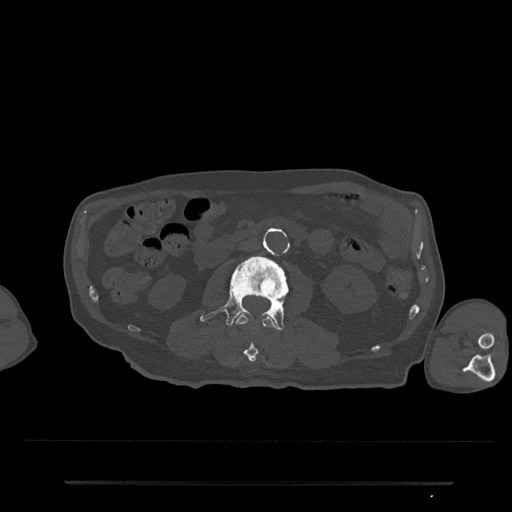
CT including the spine, one axial slice; reconstruction kernel Br40s/3; 120 kVp; bone window (W 1800 / L 400 HU); 0.5 mm slice thickness; 512 × 512 image matrix, field of view 427 × 427 mm. Male patient, age 74 years. From the clinical record (not read from this slice): primary cancer: prostate.
Outlined on this slice (semi-automatically segmented with operator editing):
- L2 vertebra: bounding box (x1, y1, x2, y2) in pixels: (234, 314, 279, 362)
- L3 vertebra: (200, 253, 303, 331)